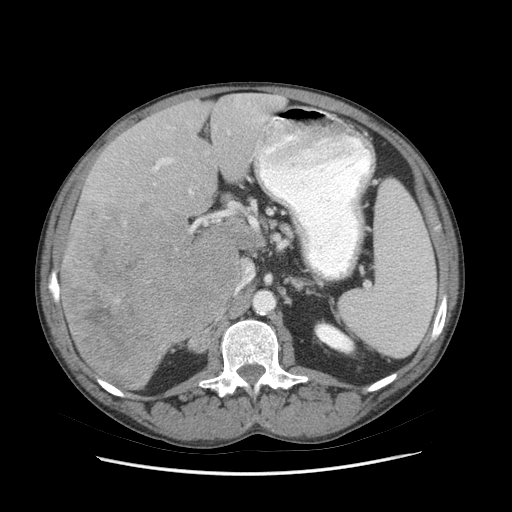
Contrast-enhanced abdominal CT (liver protocol), one axial slice. Position 42 of 89 along the scan axis. Soft-tissue window (W 400 / L 40 HU). 2.5 mm slice thickness. 512 × 512 image matrix, field of view 380 × 380 mm. Case-level facts recorded for this patient, not image findings: diagnosis: hepatocellular carcinoma (patient treated with transarterial chemoembolisation; whether this scan precedes or follows treatment is not stated here); TNM stage (as recorded): Stage-IIIB; Child-Pugh class: A; tumour differentiation: moderately differentiated.
Outlined on this slice (semi-automatic segmentation, software-assisted and operator-edited):
- liver parenchyma outside the tumour (the mass and vessels are separate outlines, so this box may not span the whole liver): bounding box <60,94,285,390> (left, top, right, bottom; pixels)
- mass: <60,208,238,387>
- liver vessels: <154,103,275,292>